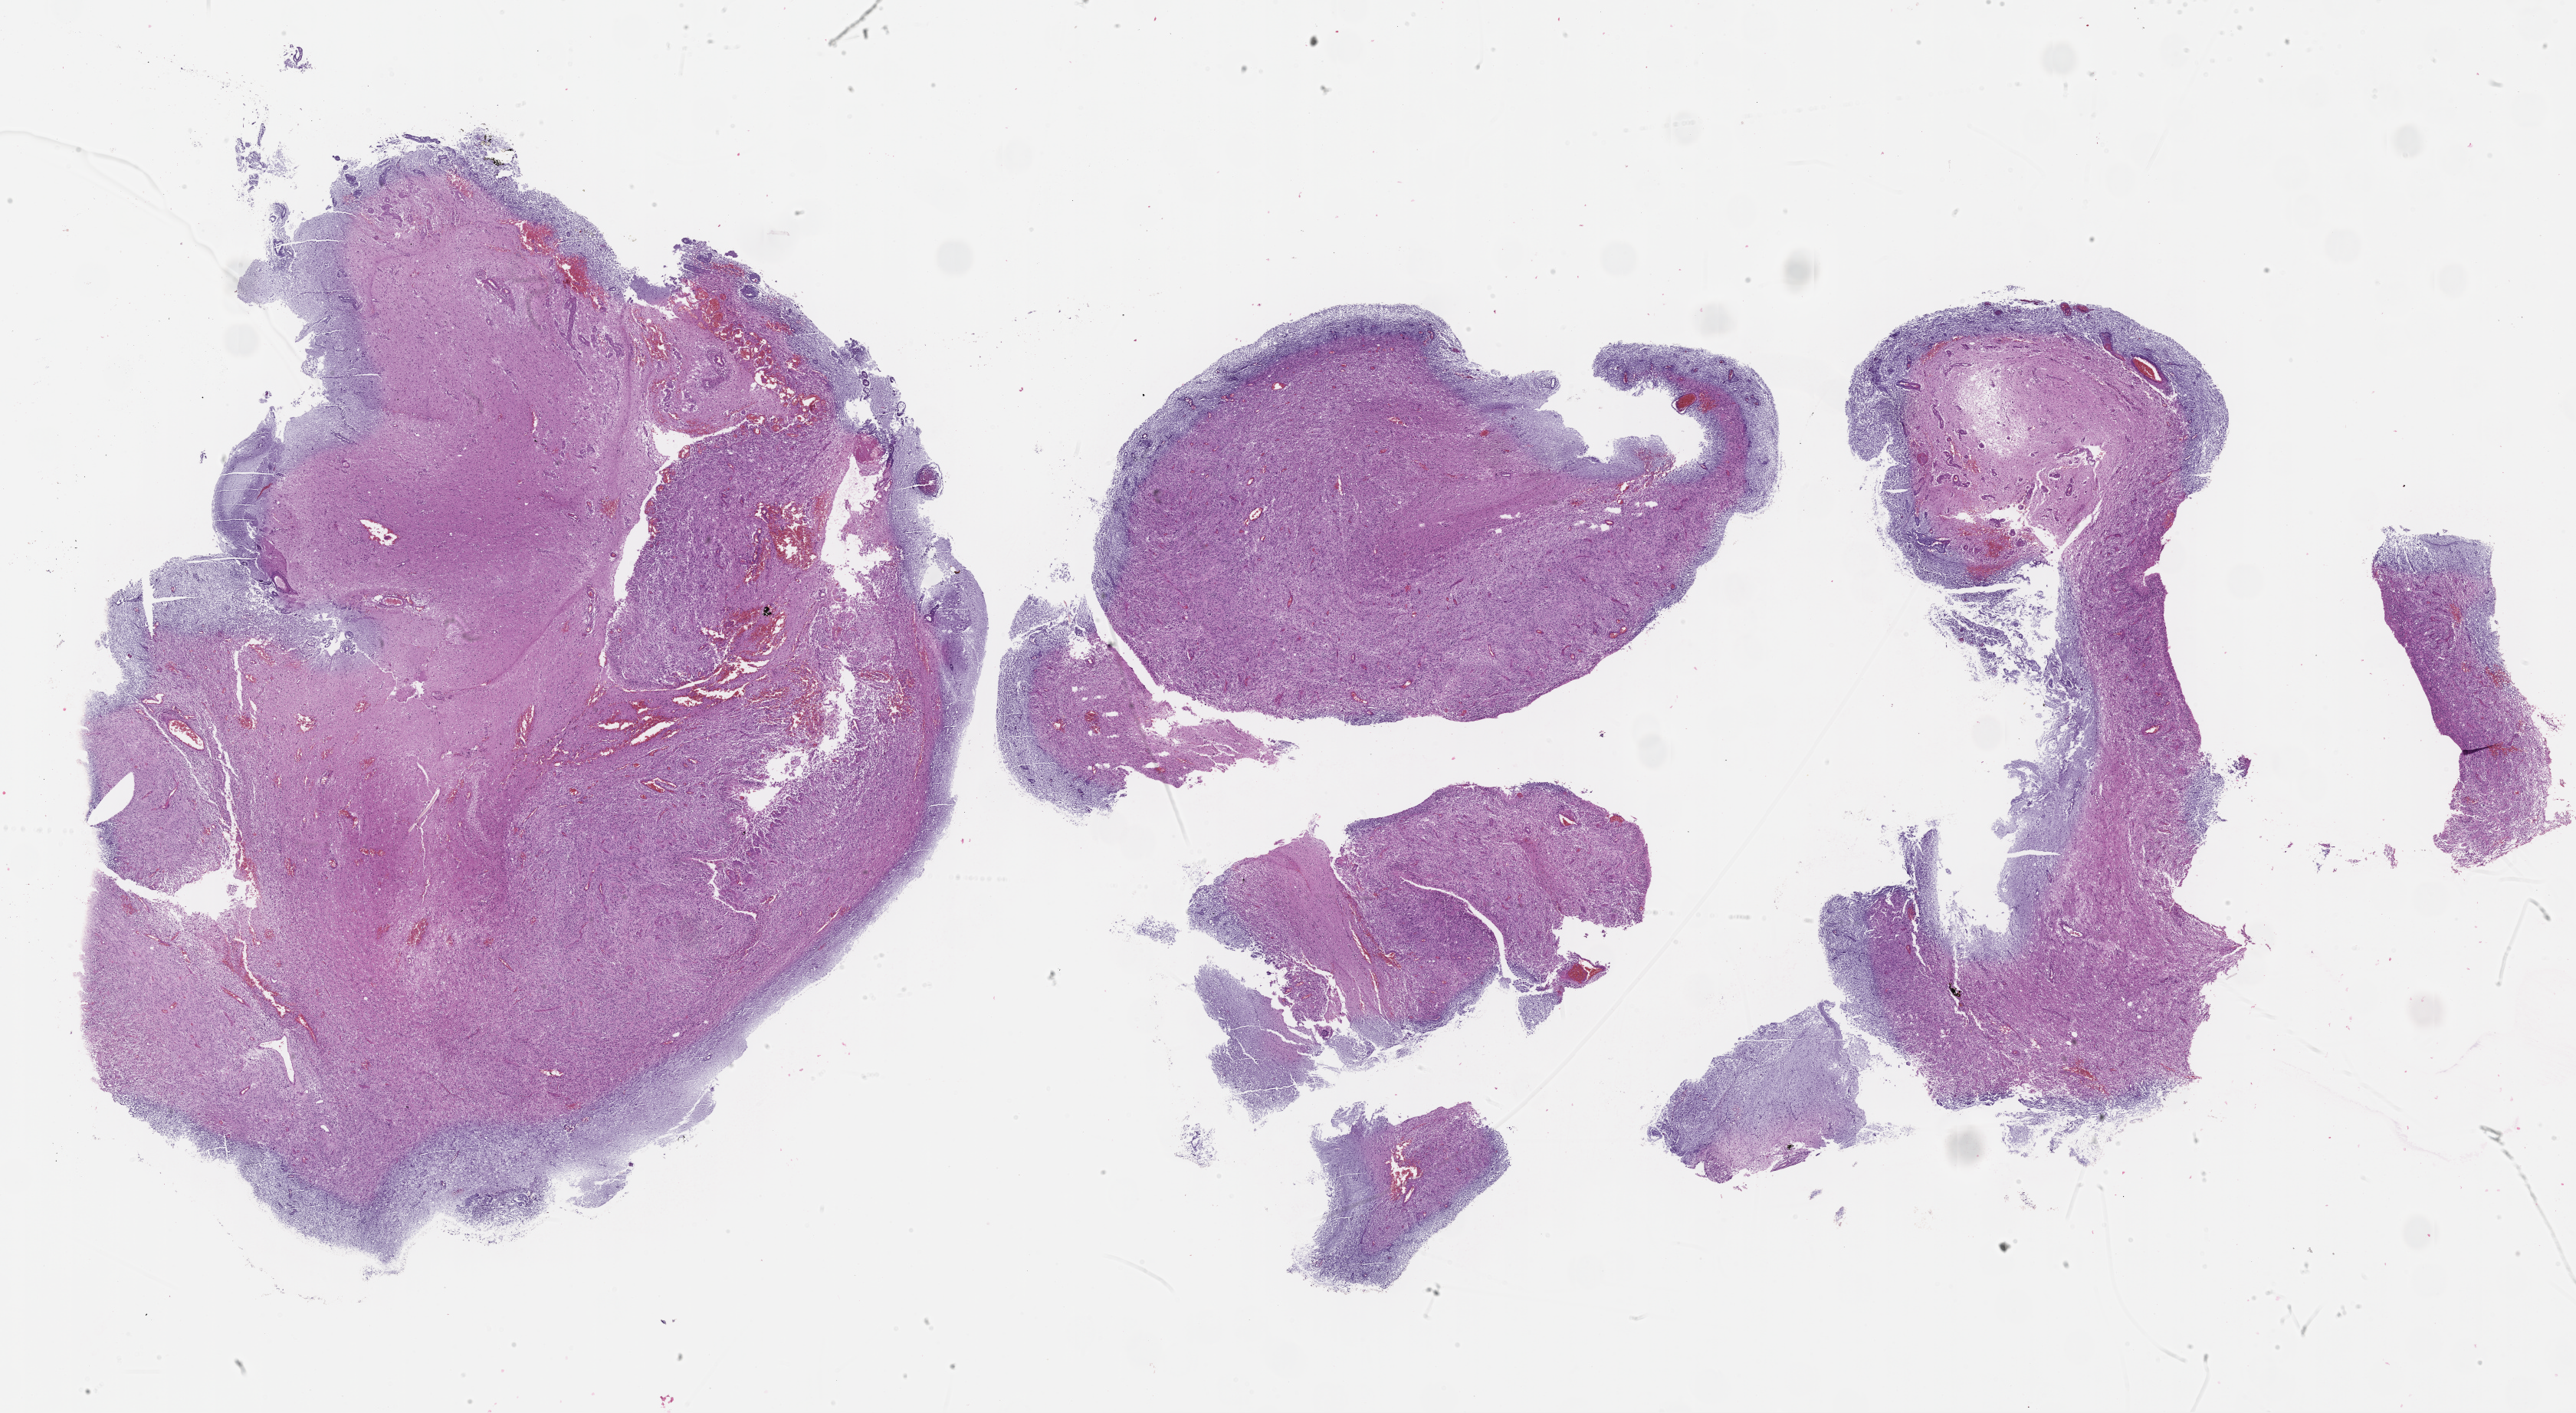
Digitized H&E tissue section (whole slide), low-resolution overview of the scanned area, about 27.2 x 14.9 mm. Formalin-fixed paraffin-embedded (FFPE) diagnostic section. Sample: primary tumour, brain. Male, age 14 years at initial diagnosis.
• diagnosis: Glioblastoma